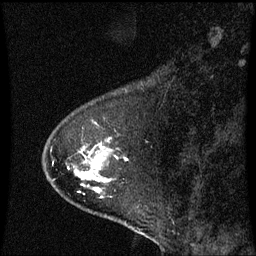
Breast MRI (dynamic contrast-enhanced), one sagittal slice. Slice 16 of 60 in the series (ordered by position). Dynamic contrast-enhanced series, image 2 of 3 at this slice position (ordered by acquisition). 1.5 T. TE 4.2 ms, TR 8.9 ms. 2 mm slice thickness. 256 × 256 image matrix. Female patient, age 53 years. From the clinical record (not read from this slice): setting: breast cancer imaged before/during neoadjuvant chemotherapy; receptor status: HR-positive, HER2-negative.
Structures marked on this image (semi-automatic segmentation, software-assisted and operator-edited):
- analysis volume of interest (the breast-tissue region the enhancement analysis was run in; not a lesion): bounding box (x1, y1, x2, y2) in pixels: (44, 122, 129, 221)
- tumour enhancement mask (voxels above the 70 % enhancement threshold inside the analysis volume of interest): (84, 164, 101, 191)